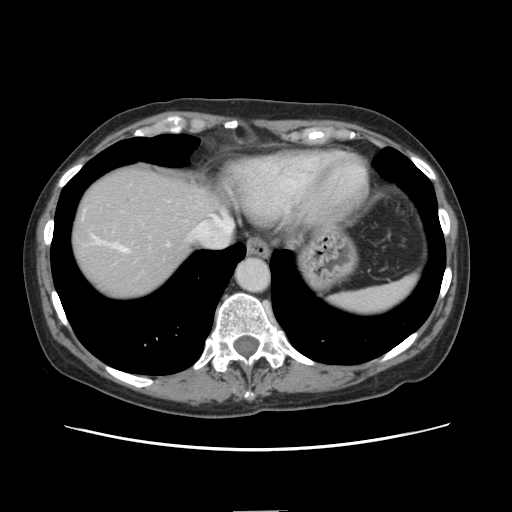
Contrast-enhanced abdominal CT, one axial slice; position 124 of 141 along the scan axis; intravenous contrast given; soft-tissue window (W 400 / L 40 HU); 2.5 mm slice thickness; 512 × 512 image matrix, field of view 350 × 350 mm. Female patient, age 63 years. From the clinical record (not read from this slice): diagnosis: colorectal cancer liver metastases, imaged before liver resection; multiple liver metastases: yes; largest metastasis: 3.2 cm; disease in both lobes: yes.
Annotated regions visible in this slice (expert manual segmentation):
- hepatic veins: bounding box <95,218,232,251> (left, top, right, bottom; pixels)
- liver: <72,163,229,301>
- planned liver remnant (the part of the liver to remain after resection): <209,195,230,226>